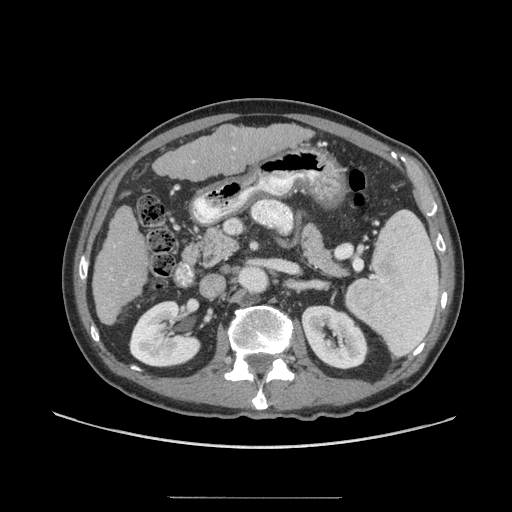
Contrast-enhanced abdominal CT (liver protocol), one axial slice. Slice 23 of 71 in the series (ordered by position). Soft-tissue window (W 400 / L 40 HU). 2.5 mm slice thickness. 512 × 512 image matrix. Case-level facts recorded for this patient, not image findings: diagnosis: hepatocellular carcinoma (patient treated with transarterial chemoembolisation; whether this scan precedes or follows treatment is not stated here); TNM stage (as recorded): Stage-I; Child-Pugh class: A; tumour nodularity: uninodular.
Outlined on this slice (semi-automatic segmentation, software-assisted and operator-edited):
- liver parenchyma outside the tumour (the mass and vessels are separate outlines, so this box may not span the whole liver): bounding box (x1, y1, x2, y2) in pixels: (92, 124, 310, 324)
- liver vessels: (111, 147, 235, 282)